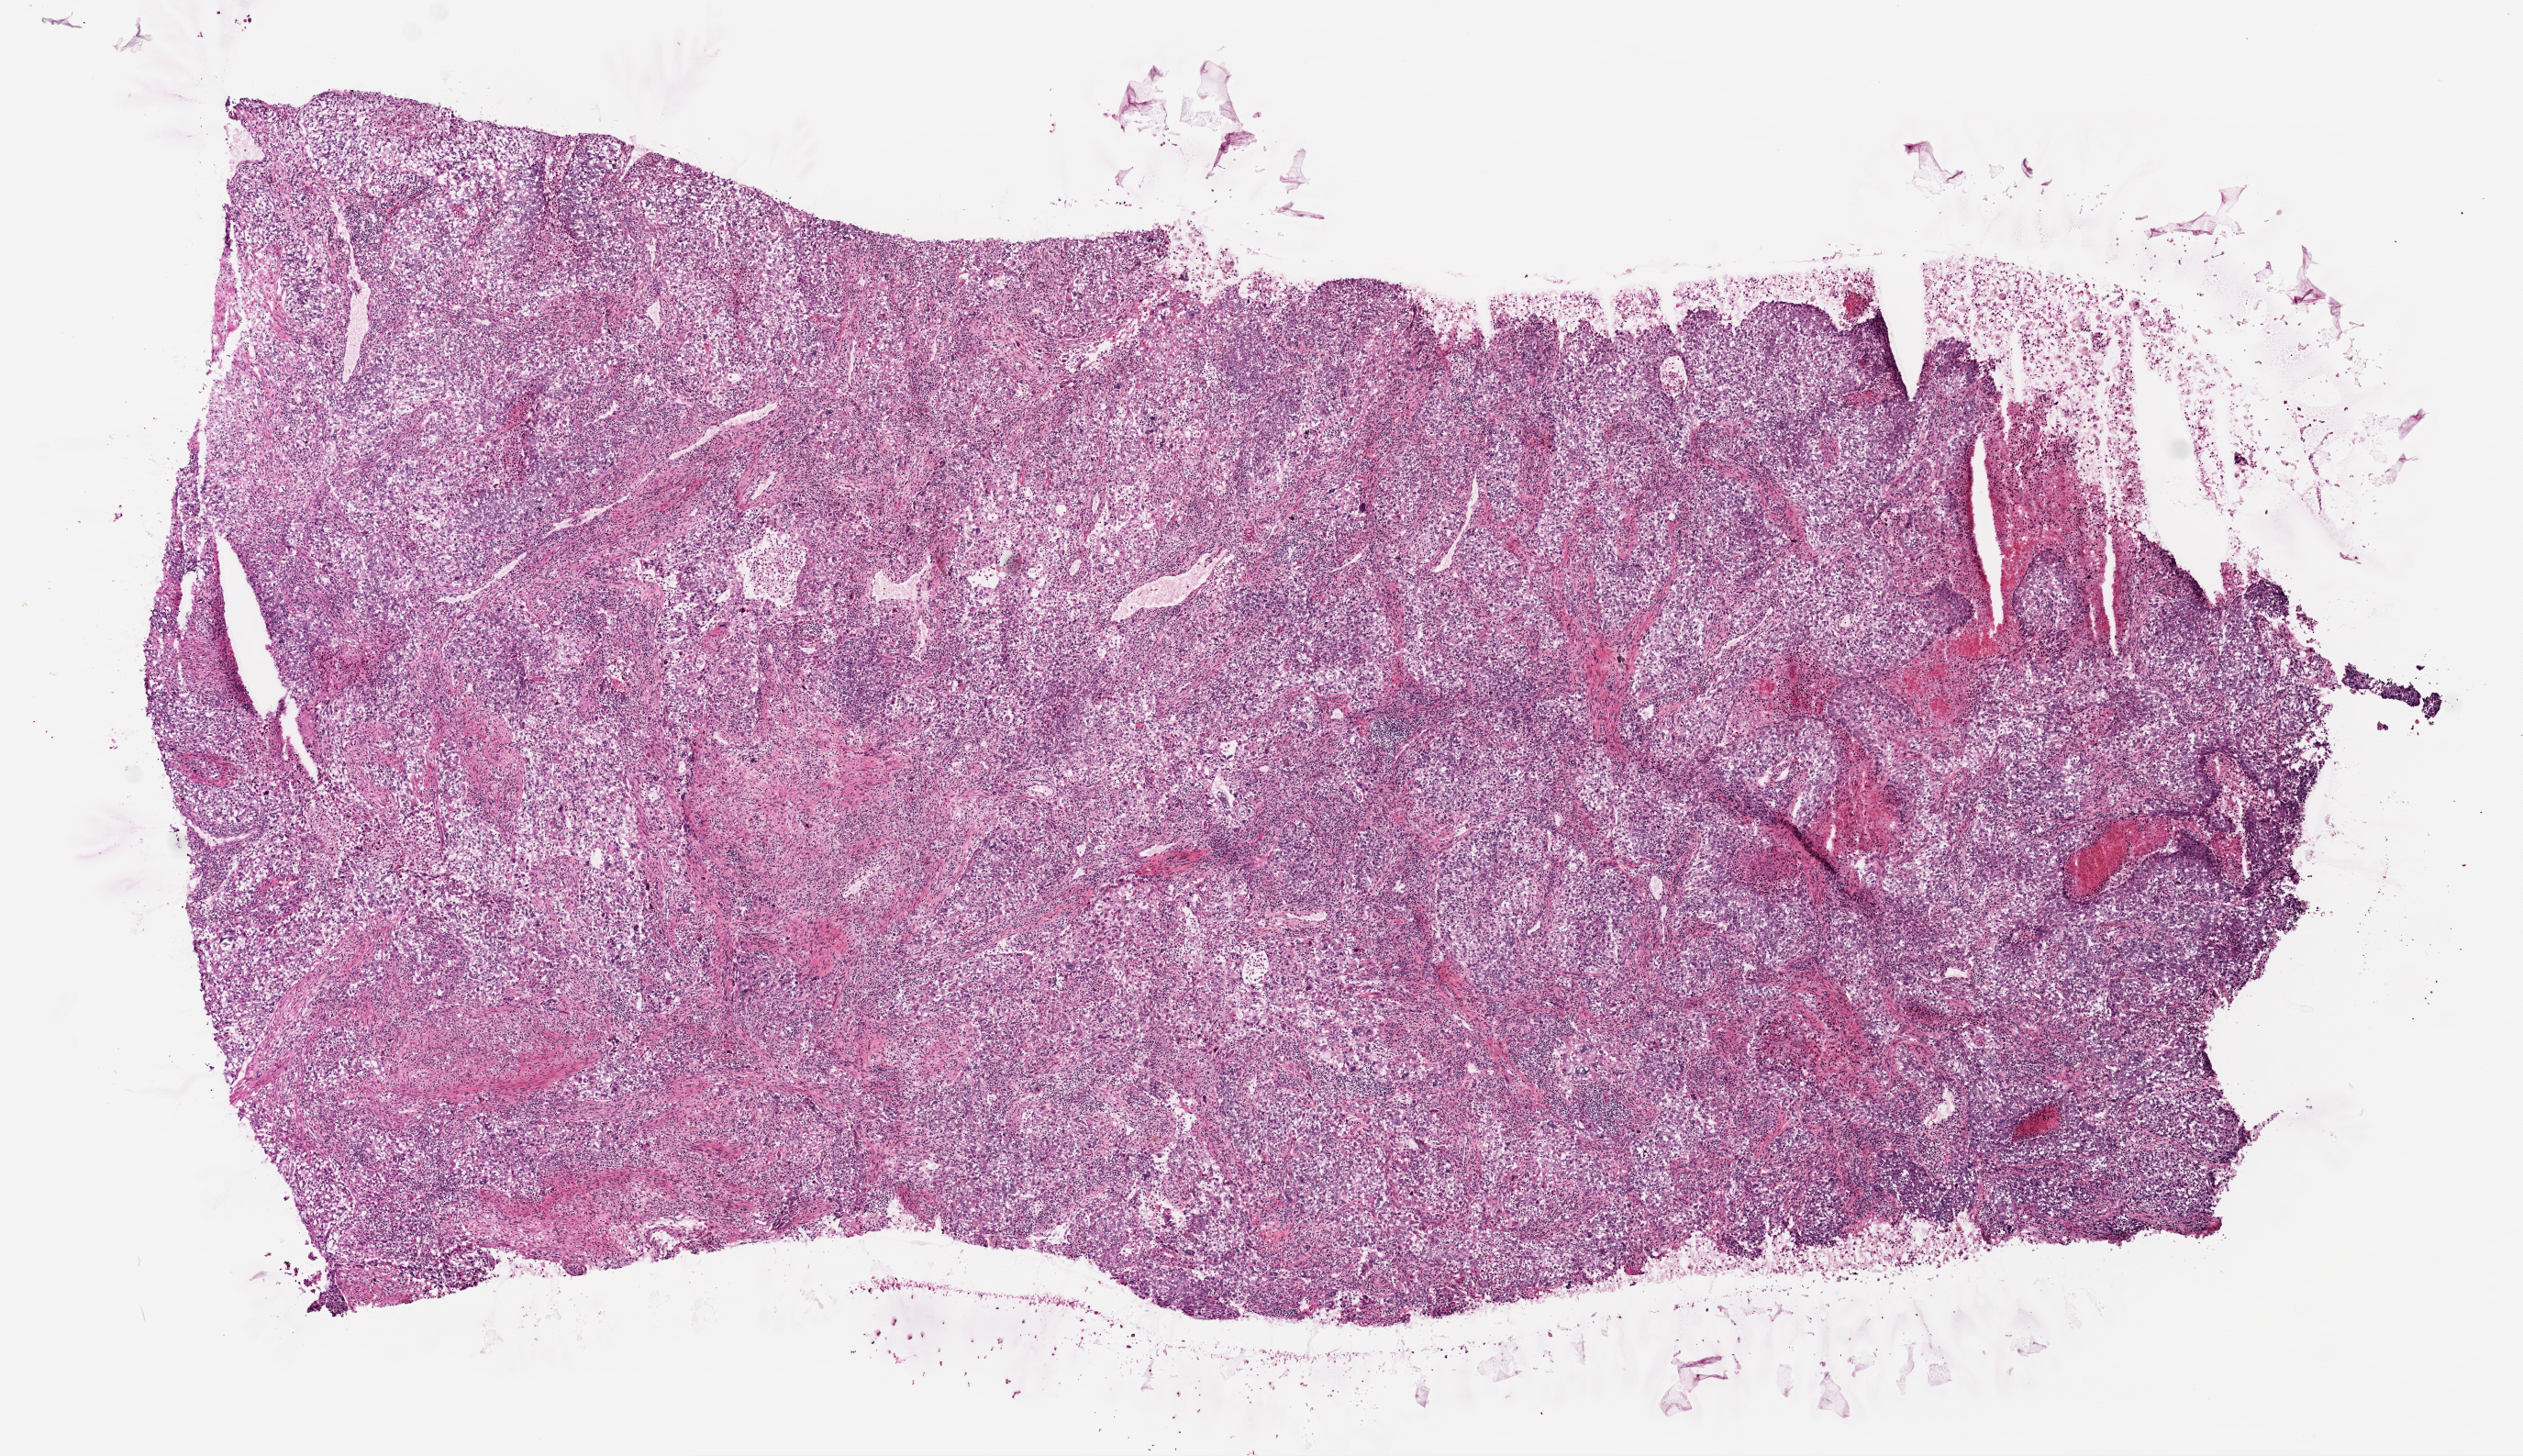
Whole-slide histology image, H&E-stained, whole scanned area (about 11.0 x 6.4 mm) shown as a low-resolution overview; frozen section from the top of the tissue portion; sample: primary tumour, lung. Male, age 38 years at initial diagnosis. Pathologist review of this section (percent, as recorded): tumour cells 80%, tumour nuclei 70%, normal cells 0%, stromal cells 15%, necrosis 5%.
* TNM: T1 N0 M0
* AJCC pathologic stage: IA
* pathologic diagnosis: Adenocarcinoma, NOS (upper lobe, lung)